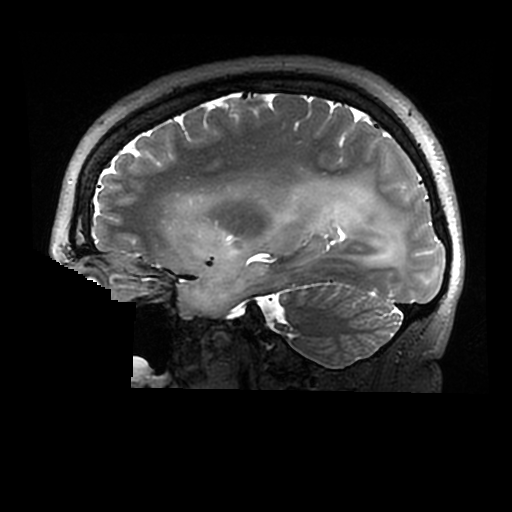
Brain MRI from a brain-tumour surgery series, one sagittal slice. Slice 193 of 320 in the series (ordered by position). 0.6 mm slice thickness. 512 × 512 image matrix, field of view 240 × 240 mm. Case-level facts recorded for this patient, not image findings: histopathology: Astrocytoma; WHO grade: 2; IDH mutation: yes.
Structures marked on this image (manually delineated by an expert):
- tumour: bounding box (x1, y1, x2, y2) in pixels: (177, 184, 406, 314)